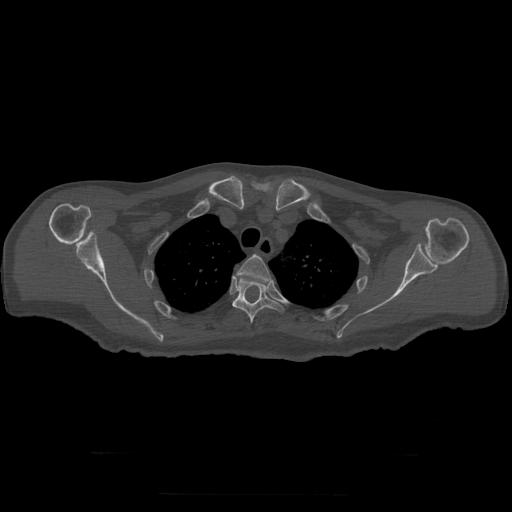
CT including the spine, one axial slice; position 246 of 397 along the scan axis; reconstruction kernel STANDARD; bone window (W 1800 / L 400 HU); 512 × 512 image matrix, field of view 510 × 510 mm. Patient age 73 years. From the clinical record (not read from this slice): primary cancer: prostate.
Outlined on this slice (semi-automatically segmented with operator editing):
- T3 vertebra: box from (x=237, y=255) to (x=271, y=282) px
- T4 vertebra: (x=233, y=276)–(x=286, y=324)